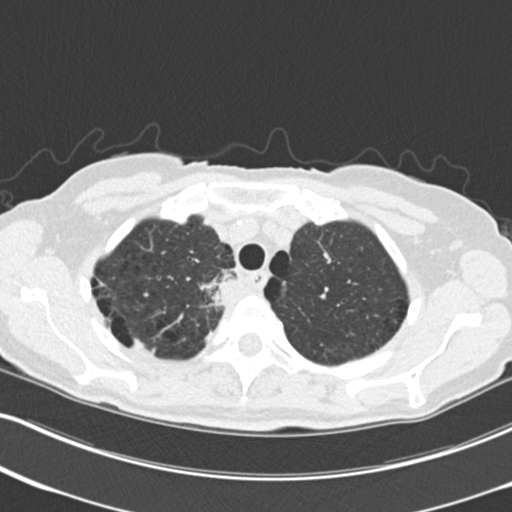
Low-dose screening chest CT, axial slice, third screening round (two years after baseline), lung window (W 1500 / L -600 HU), 2 mm slice thickness, standard (soft-tissue) reconstruction kernel (B30f), slice 43 of 226 in the series, 512 × 512 image matrix, field of view 322 × 322 mm. Female, age 68 years at enrolment. Current smoker at enrolment.
Lesion marked by an expert reader, bounding box (x1, y1, x2, y2) in pixels: (200, 262, 252, 318). Screening reader's record for this exam (one nodule recorded; not confirmed to be the boxed lesion): non-calcified nodule or mass ≥4 mm, right upper lobe, 31 × 29 mm, poorly defined margins, soft tissue attenuation, pre-existing on the prior screen: no. Official screen result: positive, other. Lung cancer was diagnosed 79 days after this screen: squamous cell carcinoma, NOS, right upper lobe, mediastinum, poorly differentiated (G3), stage IIIB (AJCC 6th edition), 43 mm at pathology.